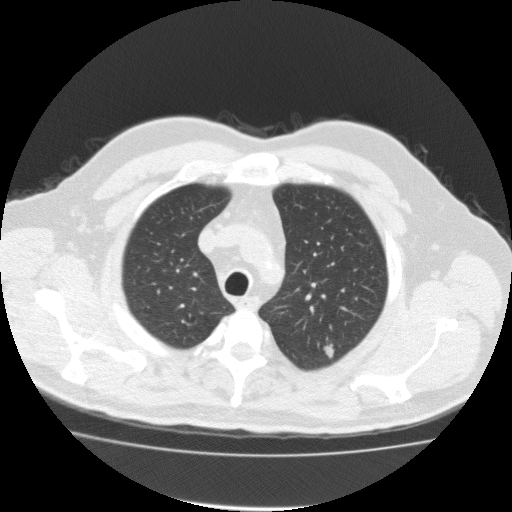
Low-dose screening chest CT, one axial slice. Slice 135 of 161 in the series (ordered by position). Reconstruction kernel FC10. 120 kVp. Lung window (W 1500 / L -600 HU). 2 mm slice thickness. 512 × 512 image matrix, field of view 412 × 412 mm.
Structures marked on this image (expert manual segmentation):
- lesion 1 (tumor, upper lobe of left lung): bounding box [x1, y1, x2, y2] px = [323, 344, 334, 358]